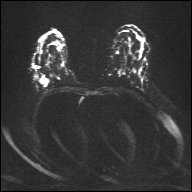
Breast MRI, one axial slice; position 20 of 32 along the scan axis; diffusion-weighted series; image 2 of 4 stored at this slice position (different b-values; order by instance number); 1.5 T; 4 mm slice thickness; 192 × 192 image matrix. Female patient.
Outlined on this slice (expert manual segmentation):
- tumour on diffusion-weighted imaging: bounding box <41,78,49,86> (left, top, right, bottom; pixels)